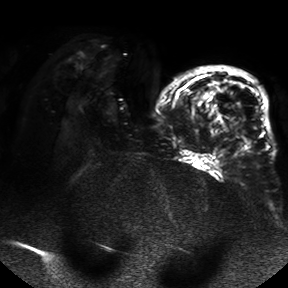
Breast MRI, one axial slice. Slice 21 of 50 in the series (ordered by position). Diffusion-weighted series; image 2 of 4 stored at this slice position (different b-values; order by instance number). 1.5 T. 4 mm slice thickness. 288 × 288 image matrix, field of view 390 × 390 mm. Female patient.
Outlined on this slice (outlined manually by an expert reader):
- tumour on diffusion-weighted imaging: bounding box <232,105,243,136> (left, top, right, bottom; pixels)